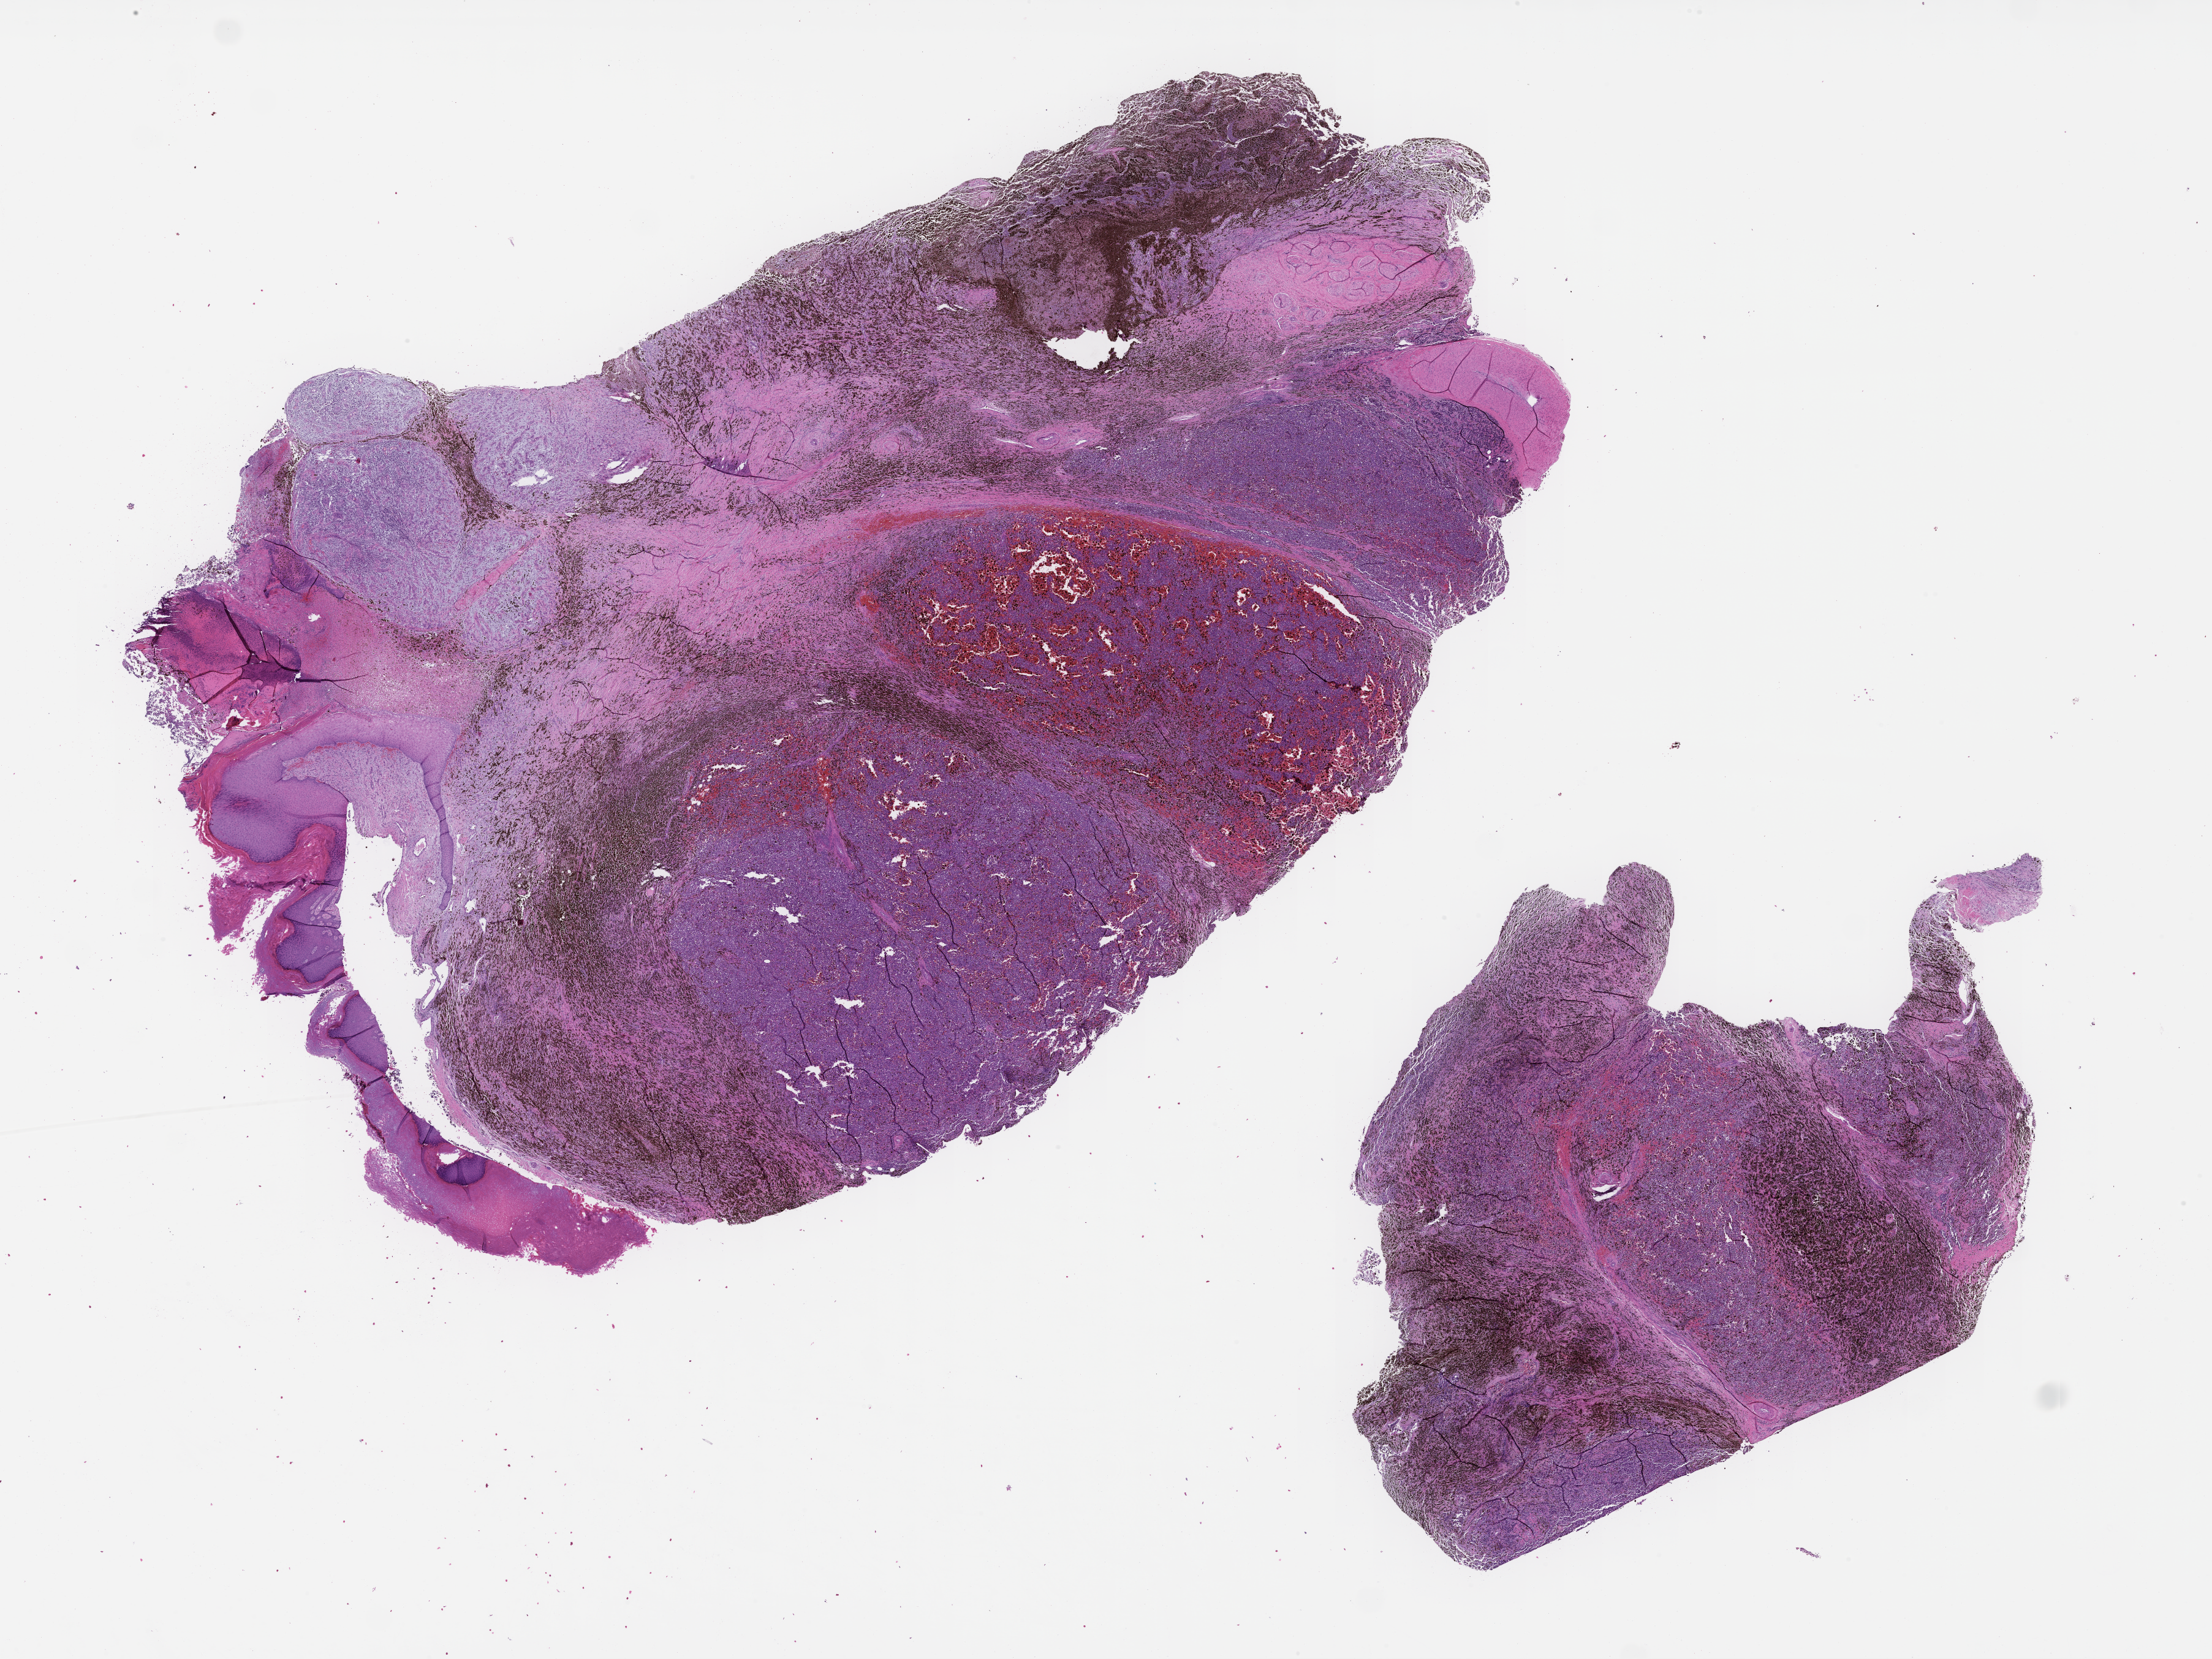
Hematoxylin and eosin (H&E) whole-slide image — shown as a low-resolution overview of the whole scanned area (about 29.1 x 21.9 mm), FFPE section, tissue site: skin, collected at baseline (before treatment). Male patient.
This section: primary tumor. Diagnosis: Melanoma.